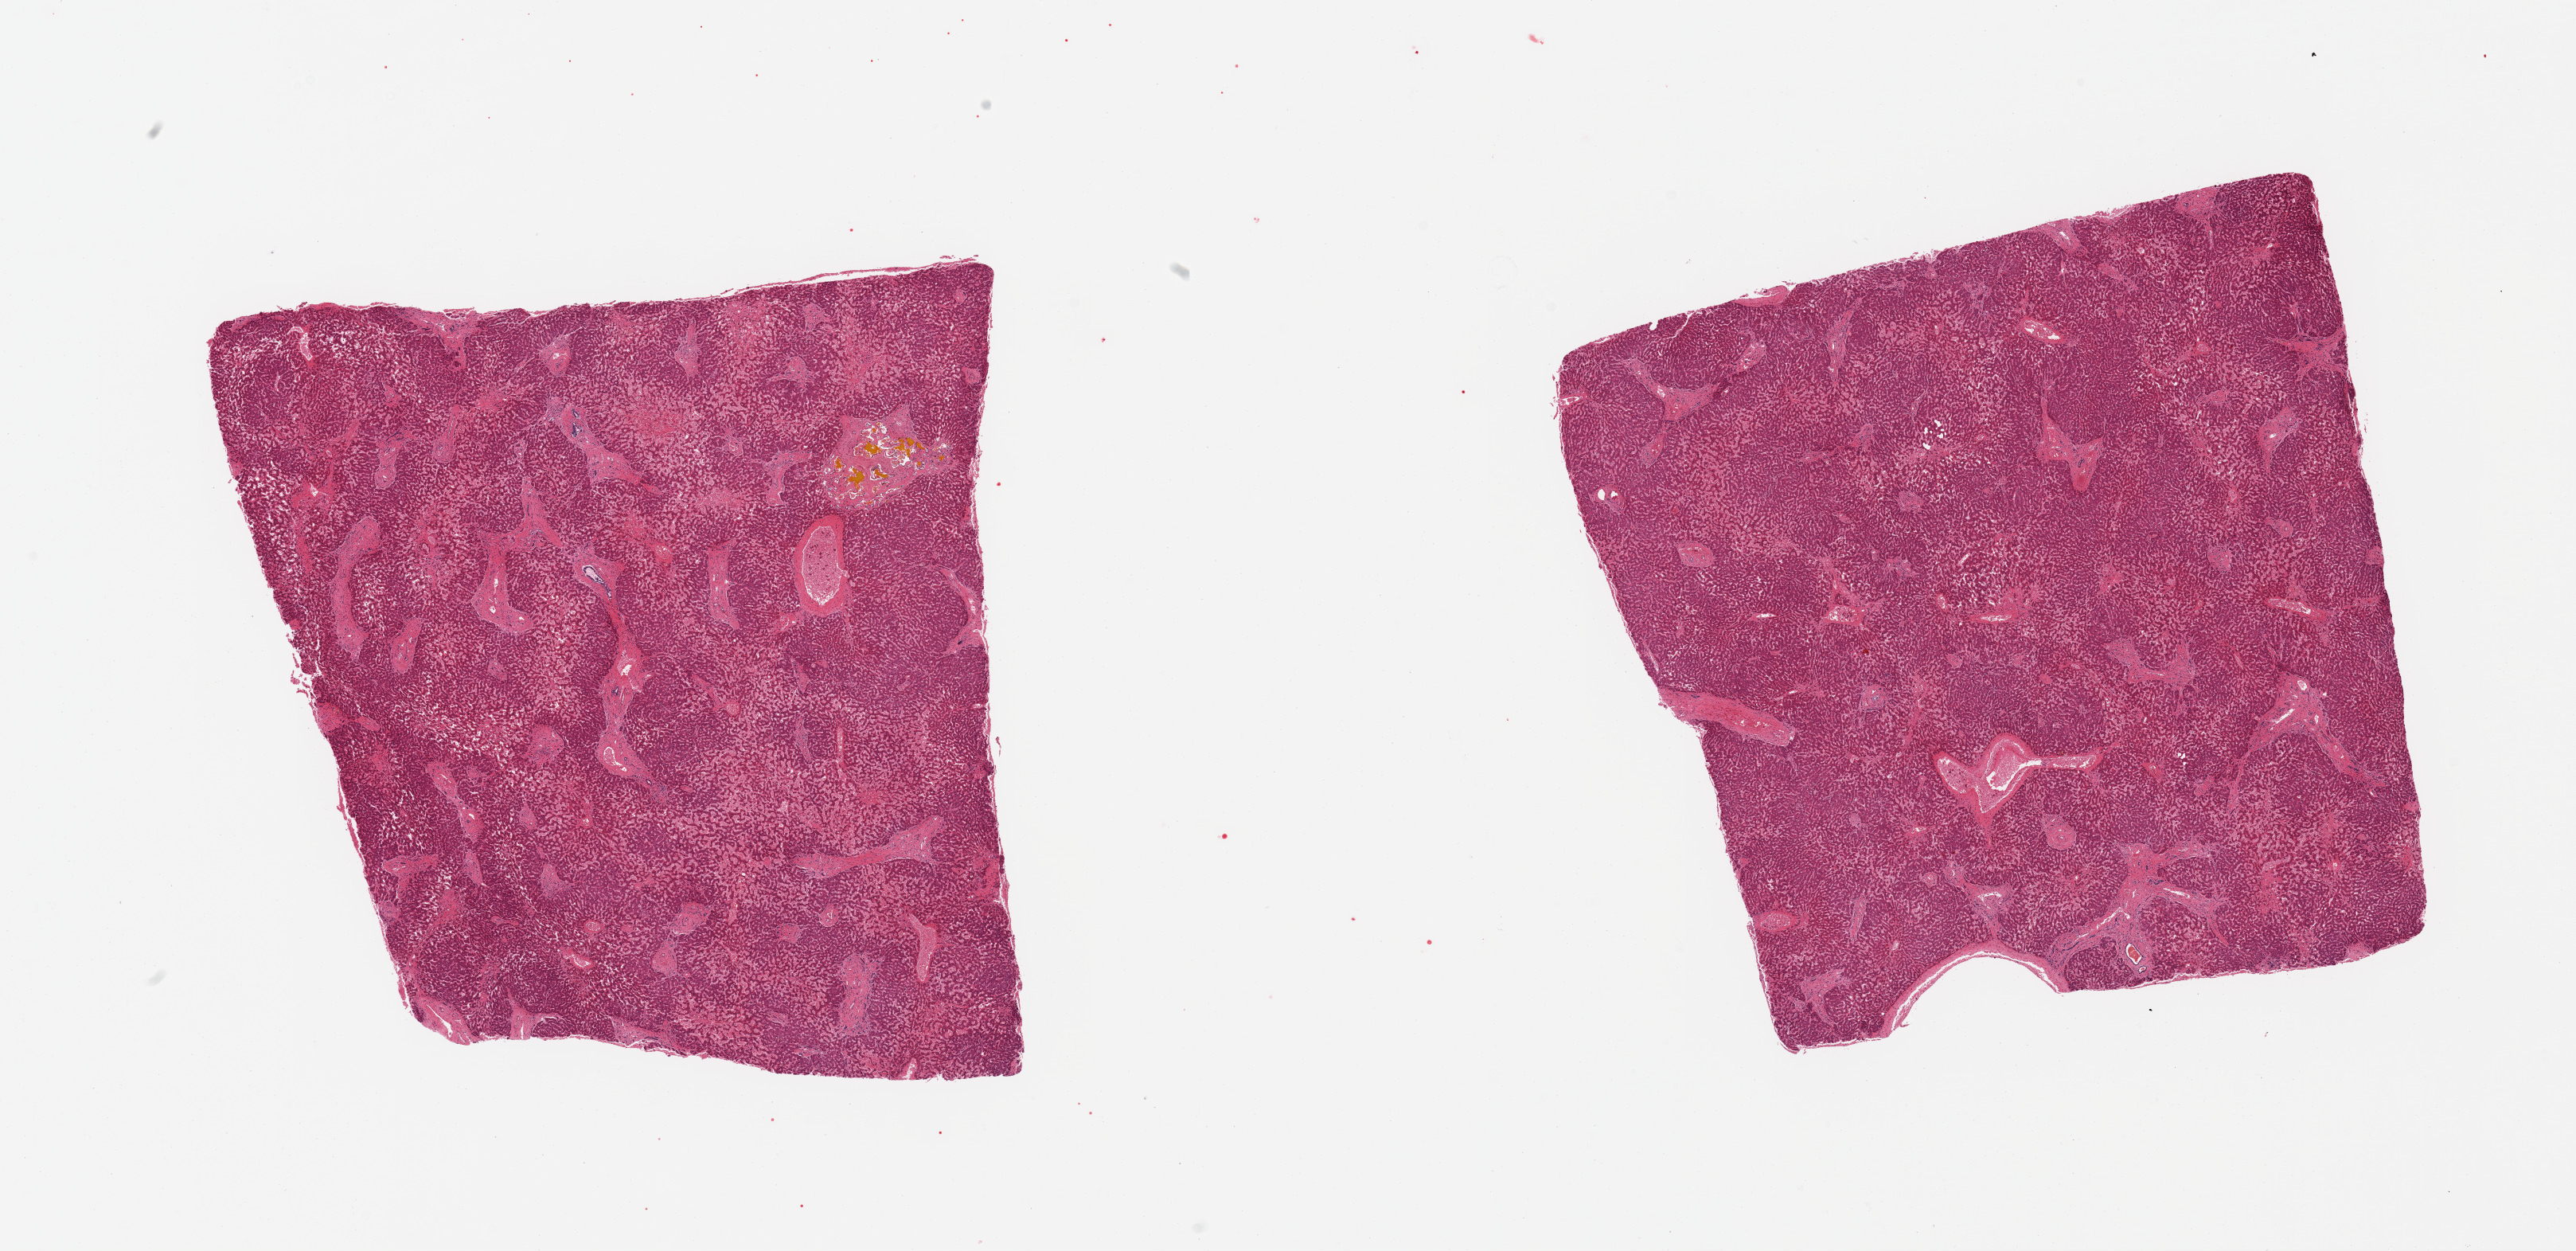
Digitized H&E-stained section — whole scanned area (about 25.6 x 12.4 mm) shown as a low-resolution overview; PAXgene-fixed paraffin-embedded (PFPE) section; section of liver (target tissue); tissue donor sample. Donor sex: male.
Pathologist's review note for this sample: 2 pieces, moderate chronic congestion.